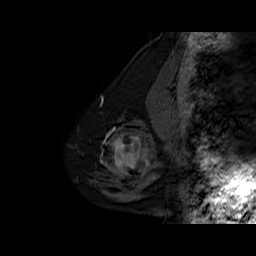
Breast MRI (dynamic contrast-enhanced), one sagittal slice; position 15 of 60 along the scan axis; dynamic contrast-enhanced series, time point 2 of 6 at this slice position (early post-contrast); 1.5 T; TE 6.3 ms, TR 32.5 ms; 4 mm slice thickness; 256 × 256 image matrix. Female patient. From the clinical record (not read from this slice): setting: breast cancer imaged before/during neoadjuvant chemotherapy; receptor status: triple-negative.
Structures marked on this image (semi-automatically segmented with operator editing):
- analysis volume of interest (the breast-tissue region the enhancement analysis was run in; not a lesion): bounding box <102,127,162,186> (left, top, right, bottom; pixels)
- tumour enhancement mask (voxels above the 100 % enhancement threshold inside the analysis volume of interest): <105,136,149,174>